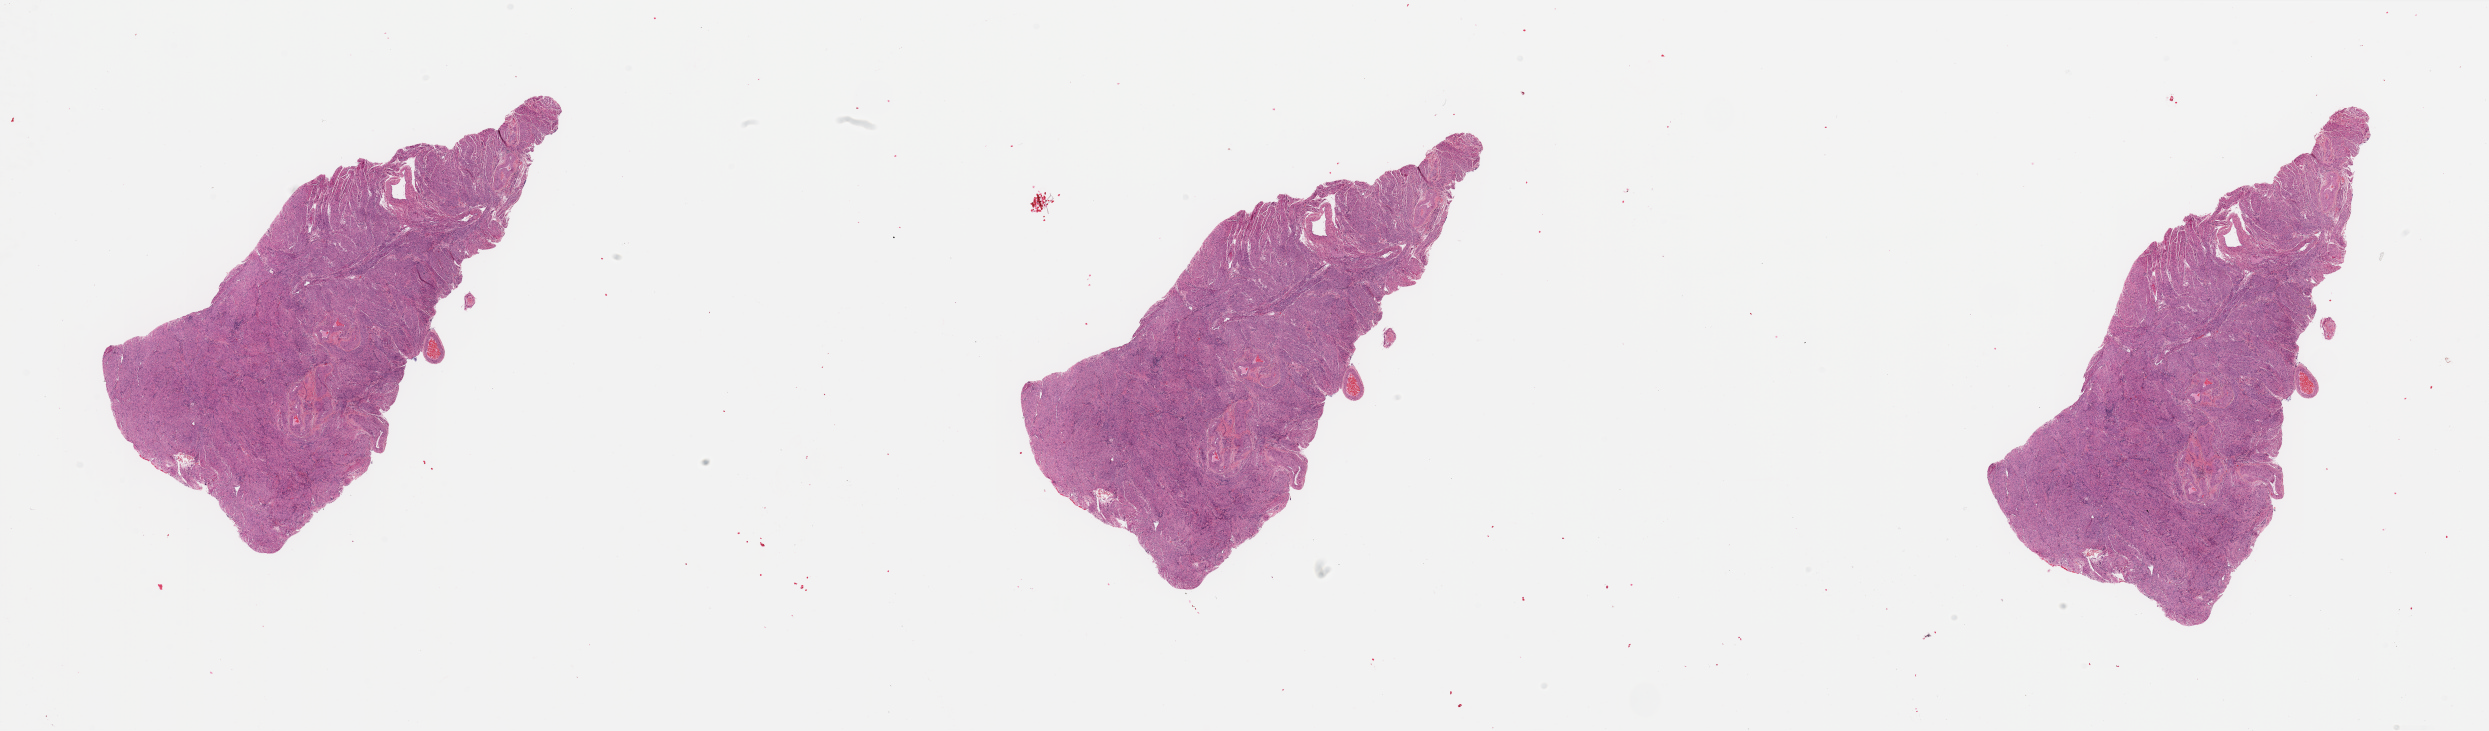
Whole-slide histology image, Hematoxylin and eosin (H&E) stained — whole scanned area (about 39.4 x 11.6 mm, from a 20x scan) shown as a low-resolution overview; uterus, normal (non-tumour) tissue. Female, 72 y/o.
This section: normal (non-tumour) tissue from the same patient. Patient diagnosis: Endometrioid adenocarcinoma, NOS.